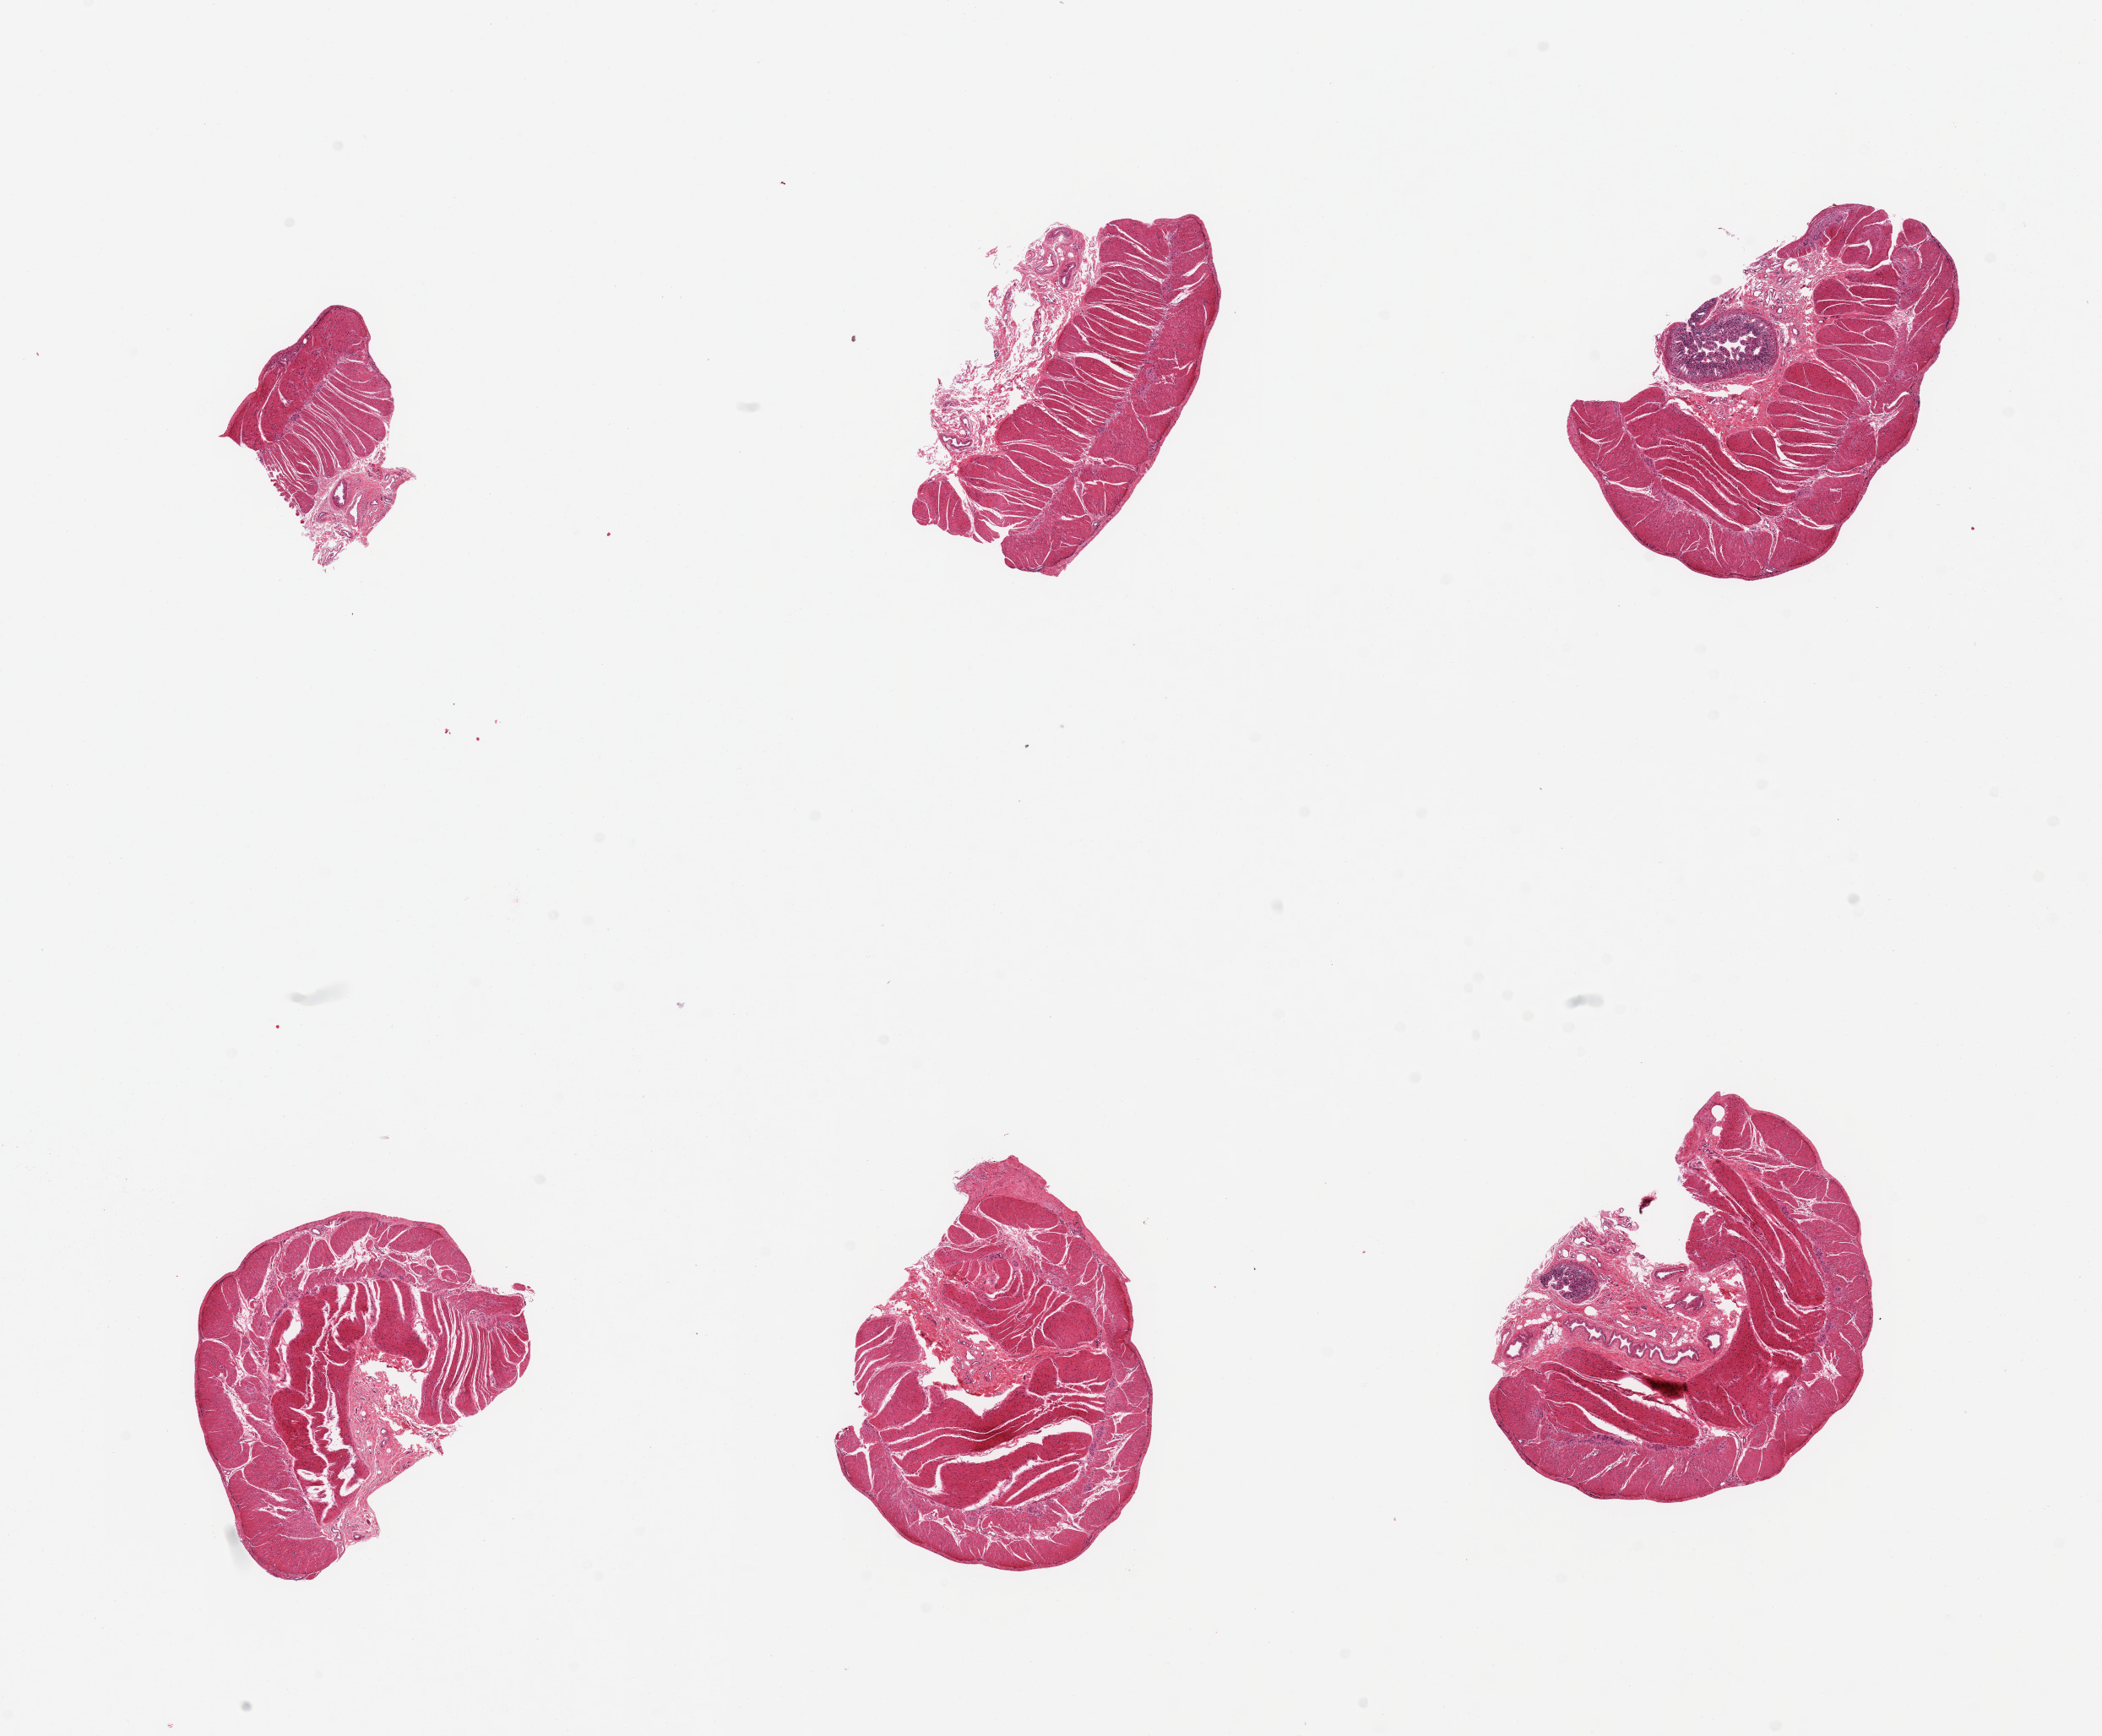
Hematoxylin and eosin (H&E) whole-slide image, a low-resolution overview of the entire scanned area, about 19.7 x 16.3 mm (slide scanned at 20x). PAXgene-fixed paraffin-embedded (PFPE) section. Sampled site (target tissue): sigmoid colon. Tissue donor sample. Donor: female.
- reviewer comment on this tissue sample: 6 pieces, trace adherent serosa or 'contaminant' autolyzed mucosa